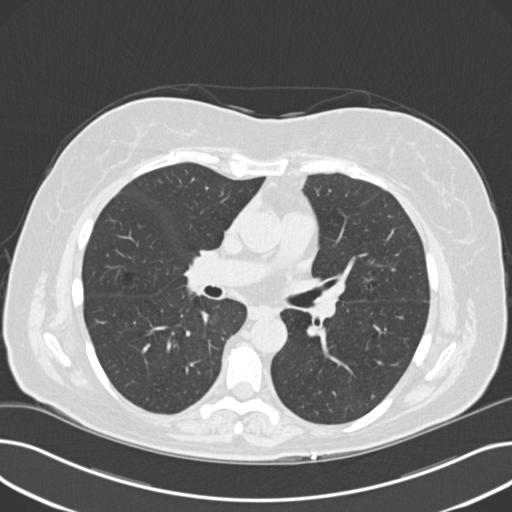
Axial slice from a low-dose chest CT screening exam; third annual screen; lung window (W 1500 / L -600 HU); 2 mm slice thickness; standard (soft-tissue) reconstruction kernel (B30f); 120 kVp. Female, age 60 years at enrolment. Current smoker at enrolment.
Lesion marked by an expert reader, bounding box (x1, y1, x2, y2) in pixels: (352, 266, 391, 301). The screening reader recorded 8 non-calcified nodules or masses ≥4 mm on this exam (right upper lobe, lingula, lingula, right middle lobe, right lower lobe, left lower lobe, left lower lobe, left lower lobe); which of them this box marks is not recorded. Official screen result: positive, other.